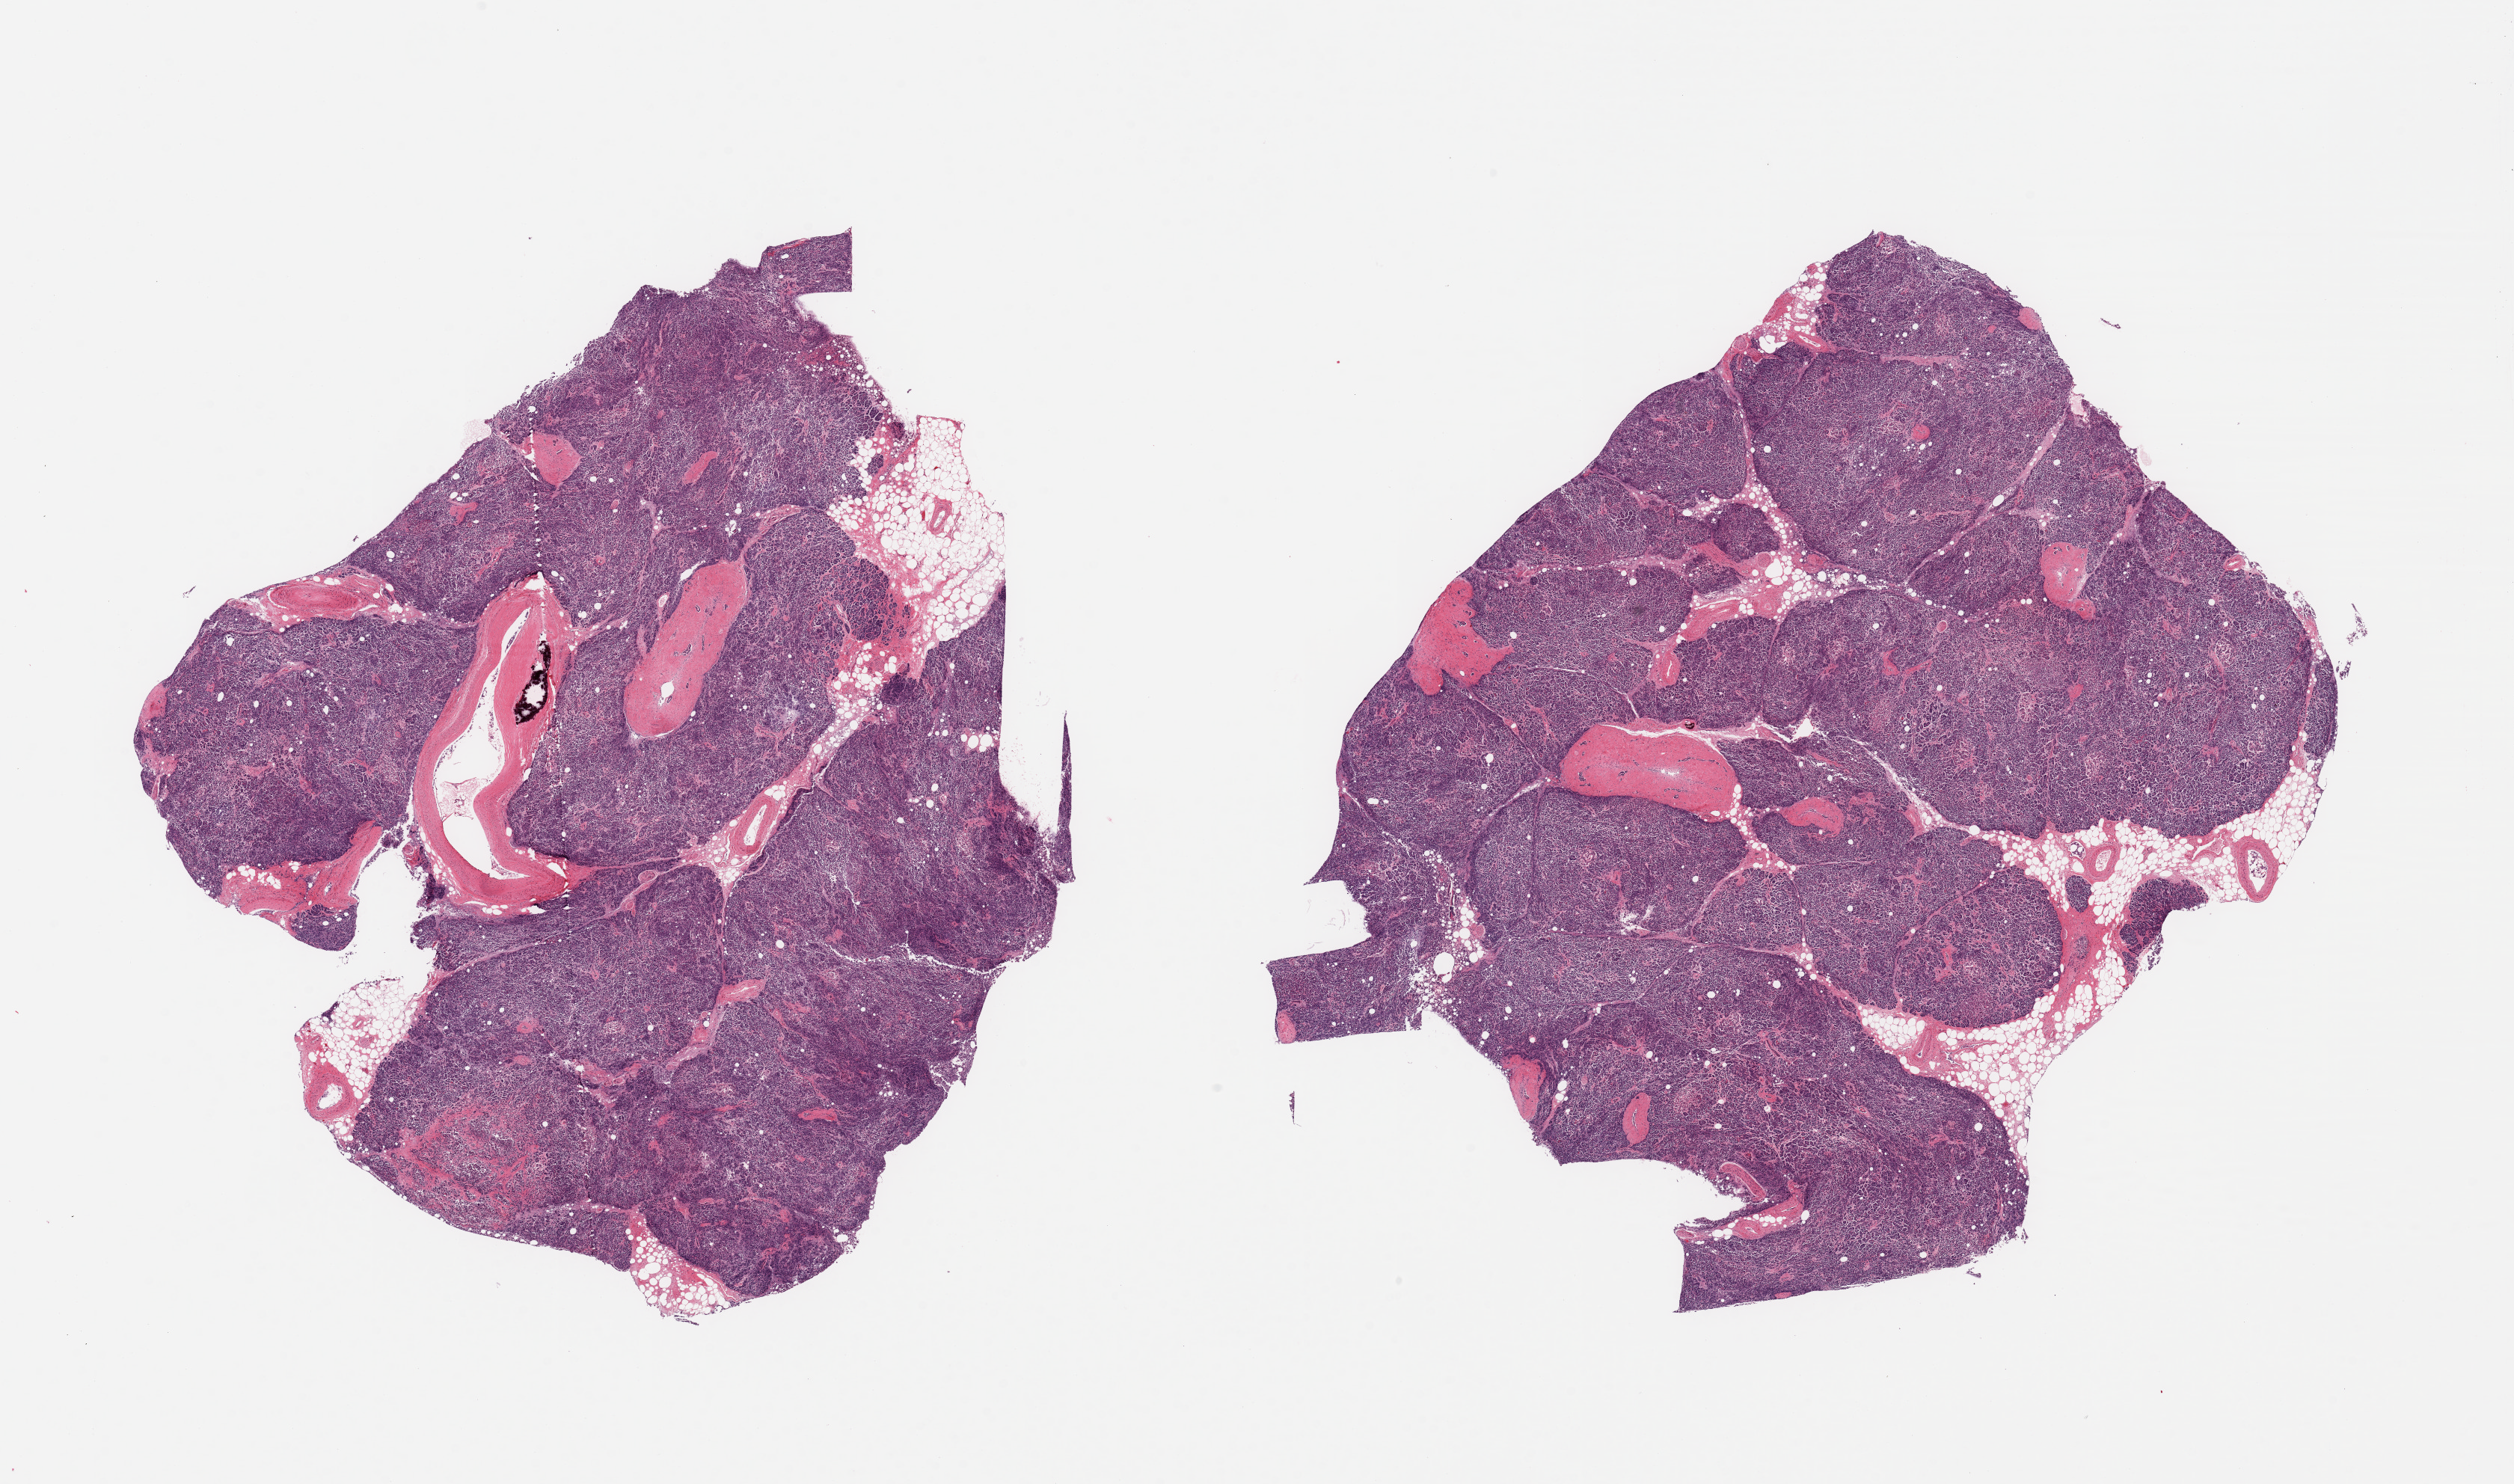
Haematoxylin and eosin whole-slide image, low-resolution overview of the scanned area, about 26.6 x 15.7 mm (acquisition: 20x scan). PAXgene-fixed, paraffin-embedded tissue. Target tissue: pancreas. Donor tissue sample.
Reviewer comment on this tissue sample: 2 pieces; 1 mm calcium deposit in a vessel wall plus a smaller one.